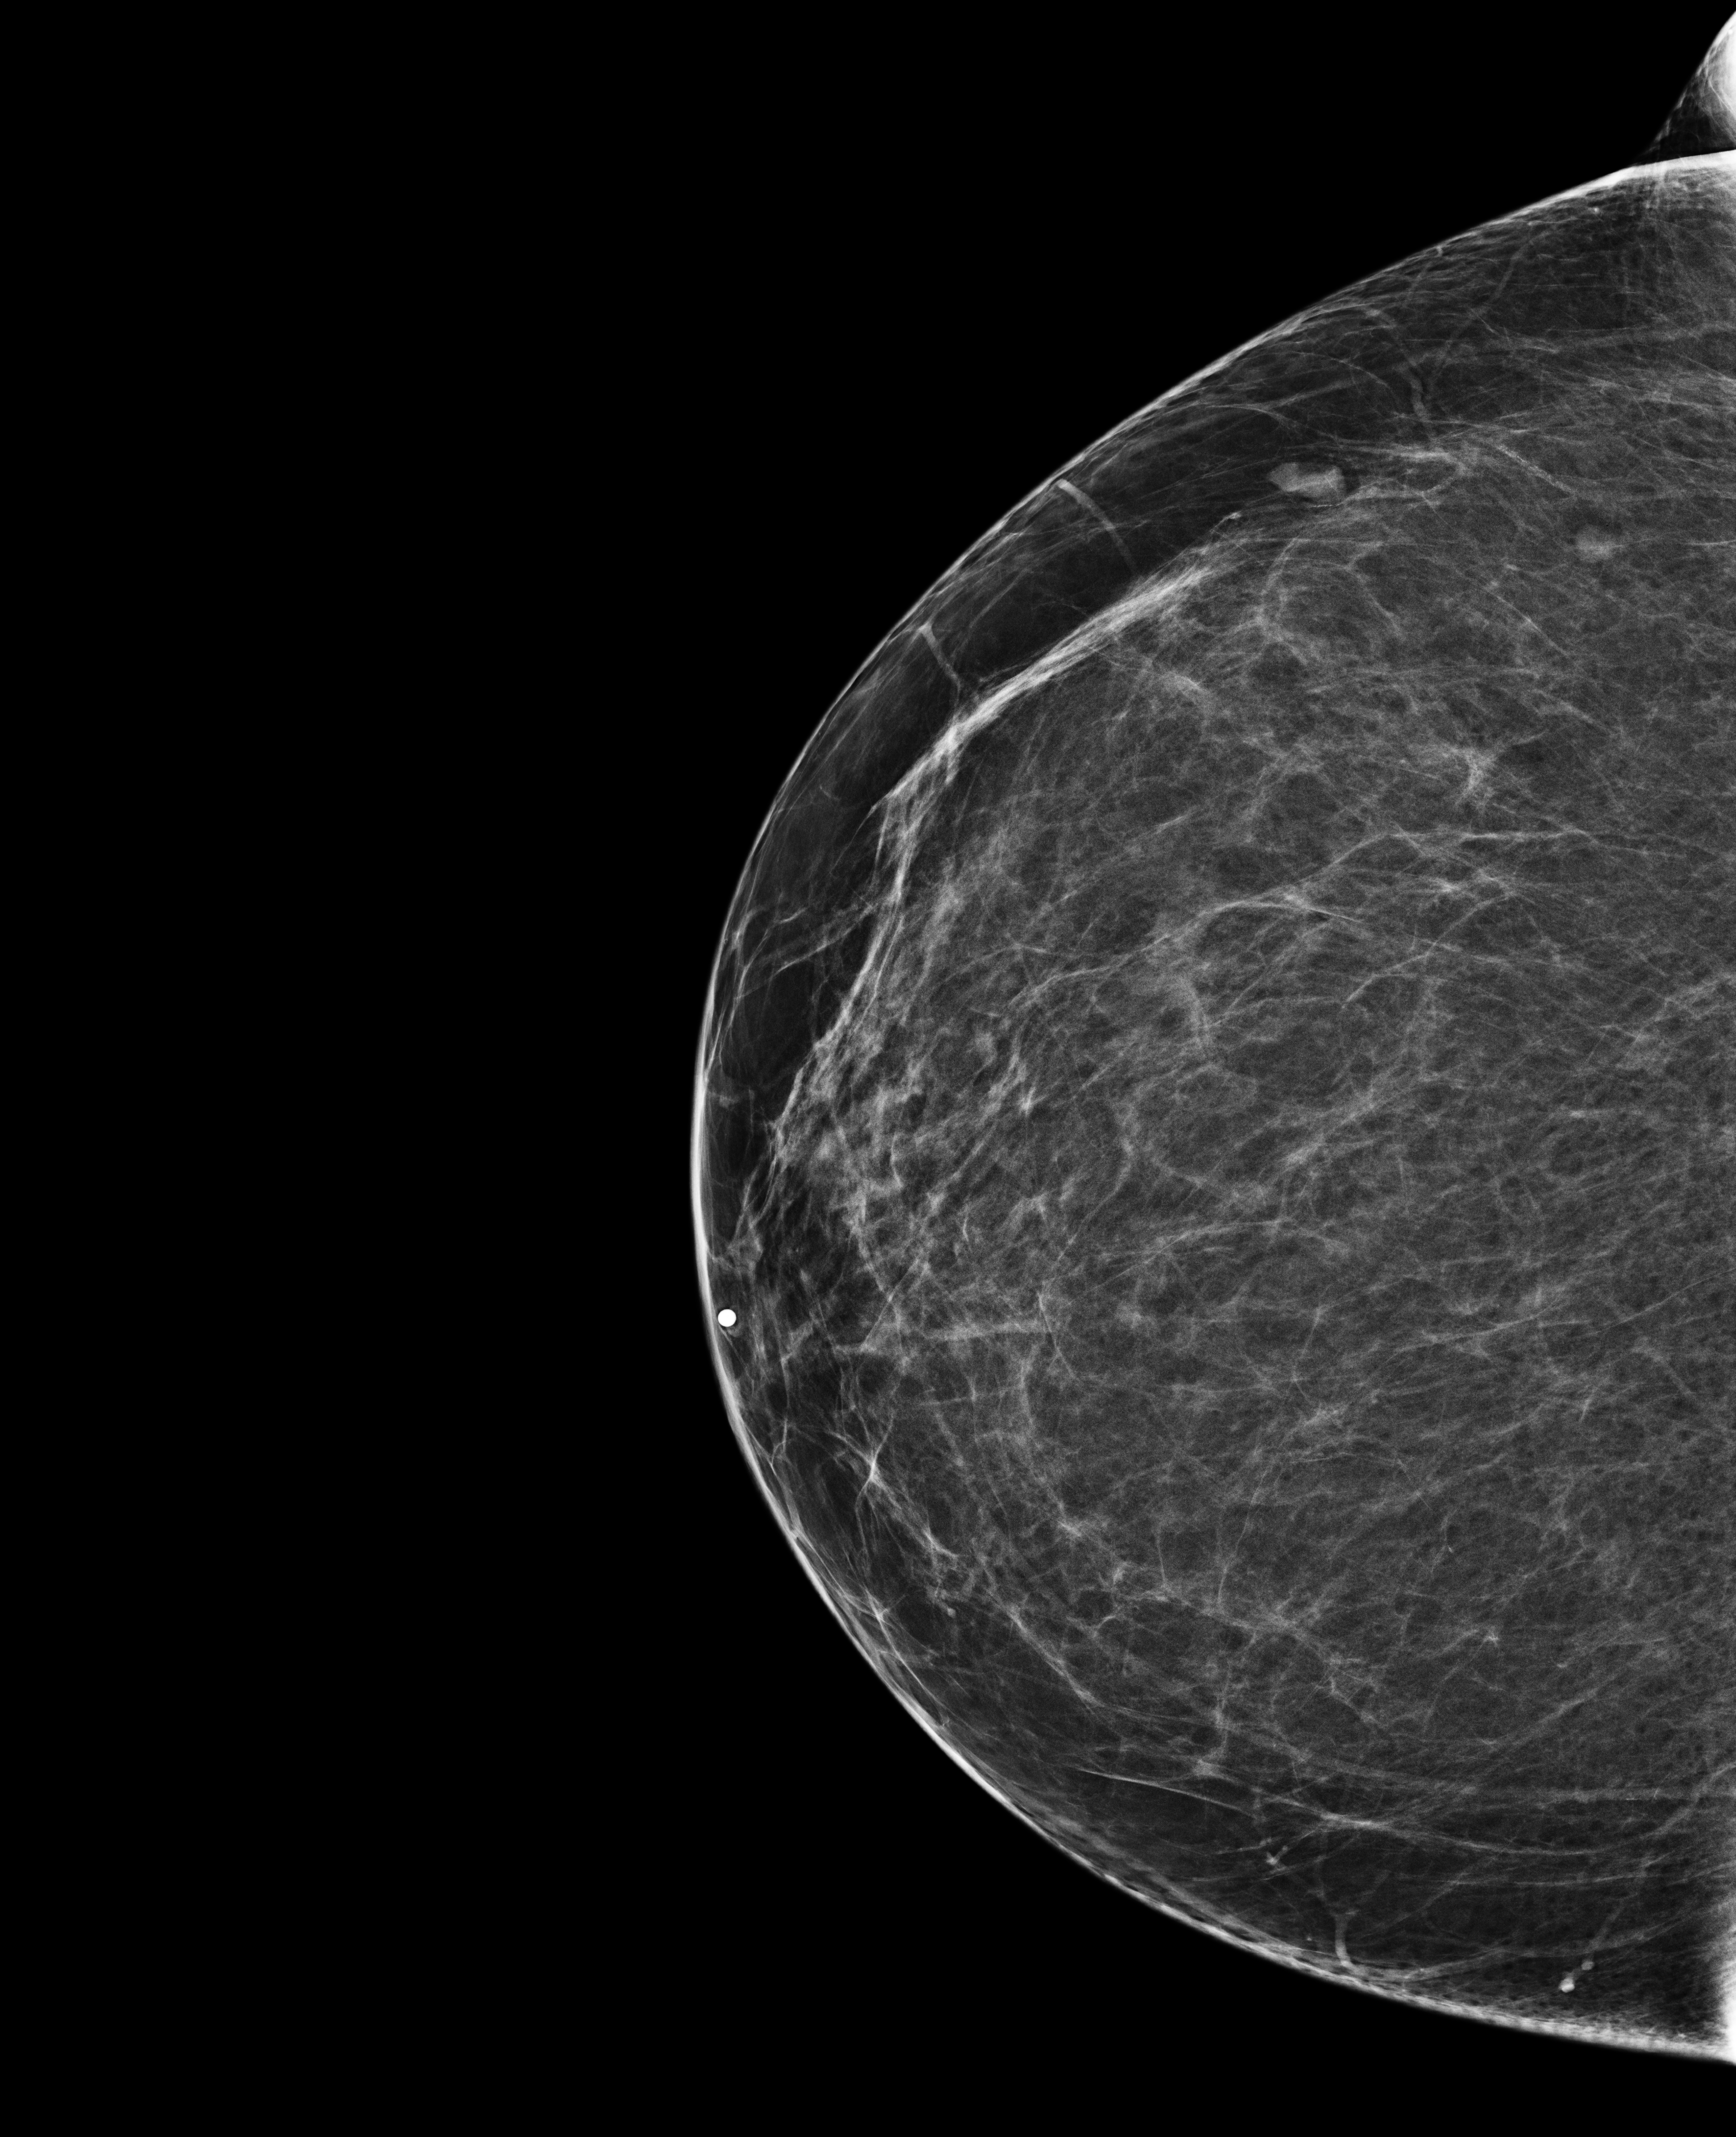
Digital mammogram (FFDM), right breast, craniocaudal (CC) view, screening examination, compressed breast thickness 69 mm. Female patient, age 52 years.
Breast density at the screening exam (both breasts): scattered fibroglandular densities (BI-RADS density category b). Final BI-RADS category for the screening round (tomosynthesis exam, both breasts): category 2. Recall: no recall after this screen.